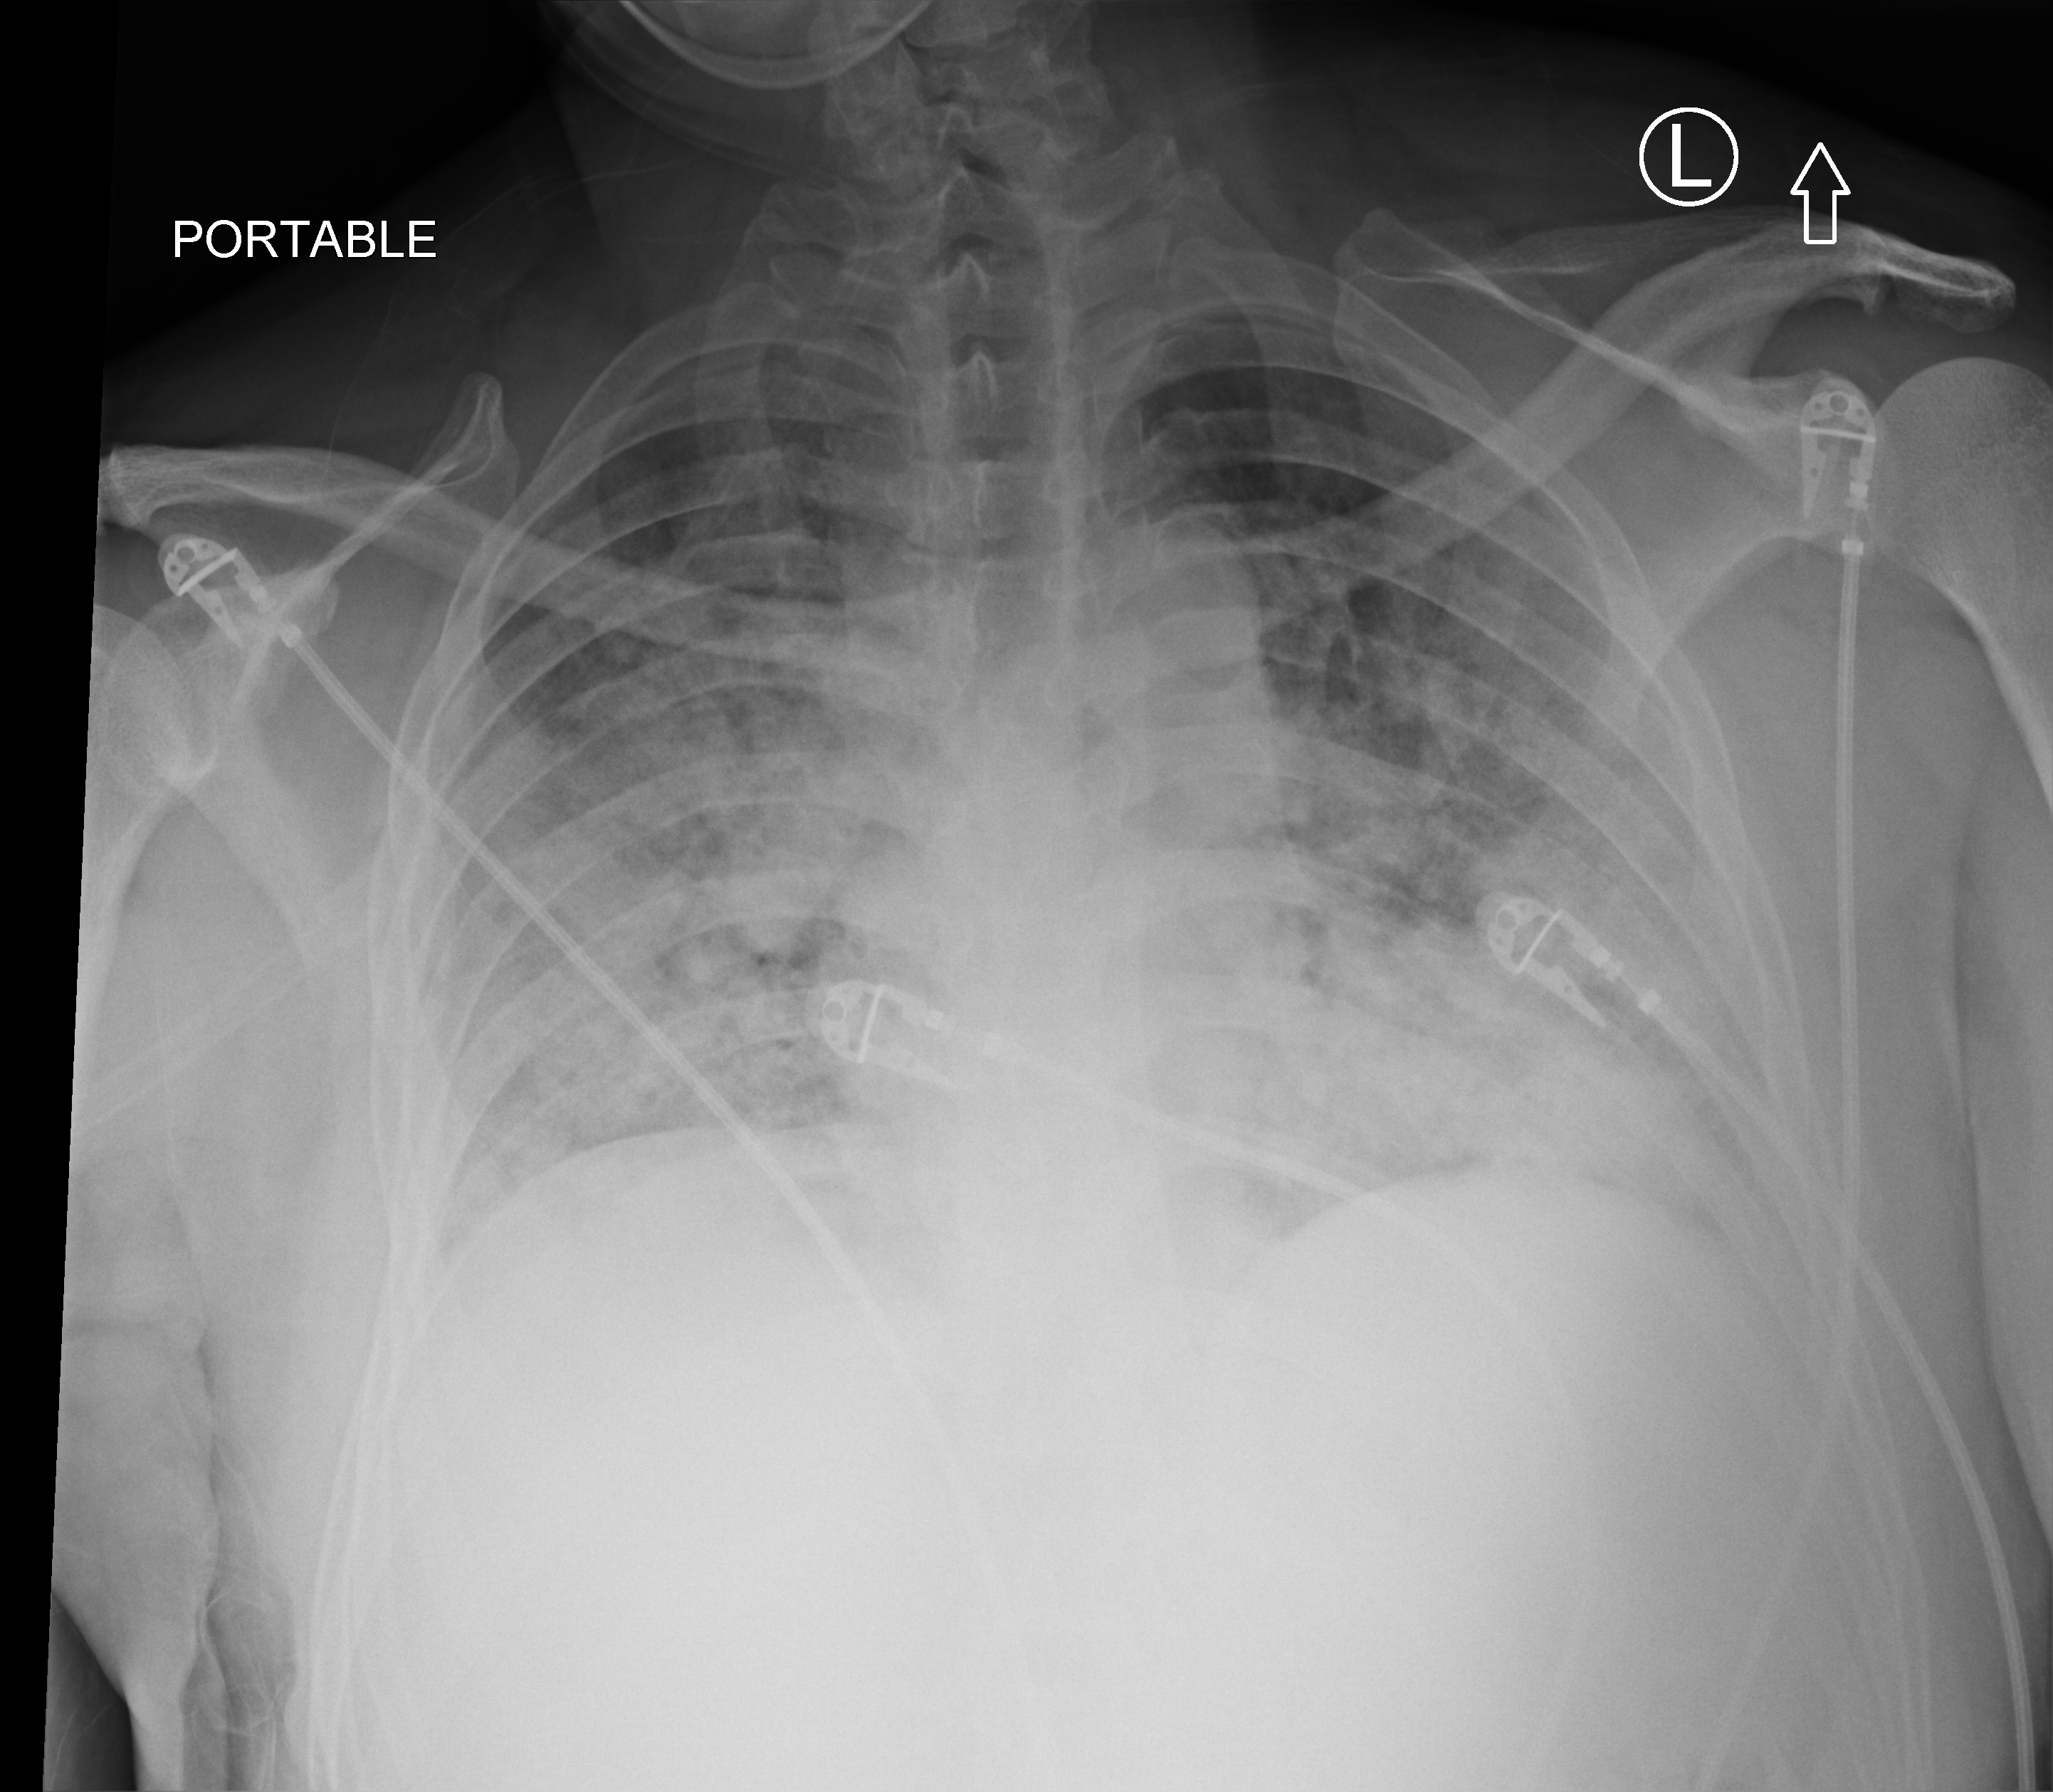
Chest X-ray (portable); anteroposterior (AP) projection. Male patient hospitalised with COVID-19, age 18–59 years.
Hospital-stay facts (about this admission, not read from this image; timing relative to this image not recorded): length of hospital stay: 14 days; admitted to intensive care during this hospital stay: no; mechanically ventilated during this hospital stay: no.